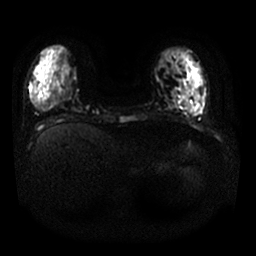
Breast MRI, one axial slice. Slice 4 of 25 in the series (ordered by position). Diffusion-weighted series; image 2 of 4 stored at this slice position (different b-values; order by instance number). 1.5 T. 4 mm slice thickness. 256 × 256 image matrix. Female patient.
Annotated regions visible in this slice (outlined manually by an expert reader):
- tumour on diffusion-weighted imaging: bounding box <190,100,192,102> (left, top, right, bottom; pixels)